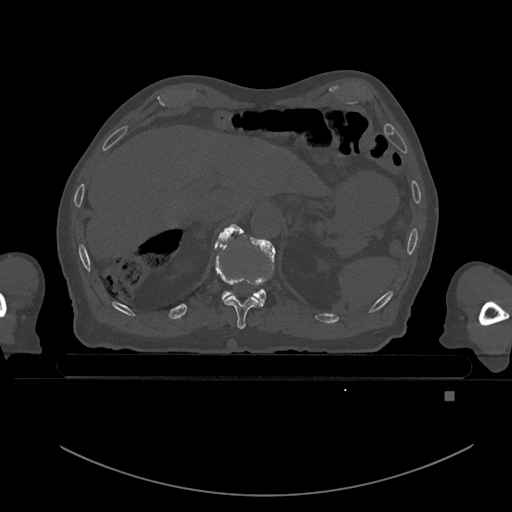
CT including the spine, one axial slice. Slice 63 of 969 in the series (ordered by position). Bone window (W 1800 / L 400 HU). 0.5 mm slice thickness. 512 × 512 image matrix. Patient: male, 82 years. Case-level facts recorded for this patient, not image findings: primary cancer: prostate.
Annotated regions visible in this slice (semi-automatic segmentation, software-assisted and operator-edited):
- T10 vertebra: bounding box <214,239,261,330> (left, top, right, bottom; pixels)
- T11 vertebra: <218,224,276,306>